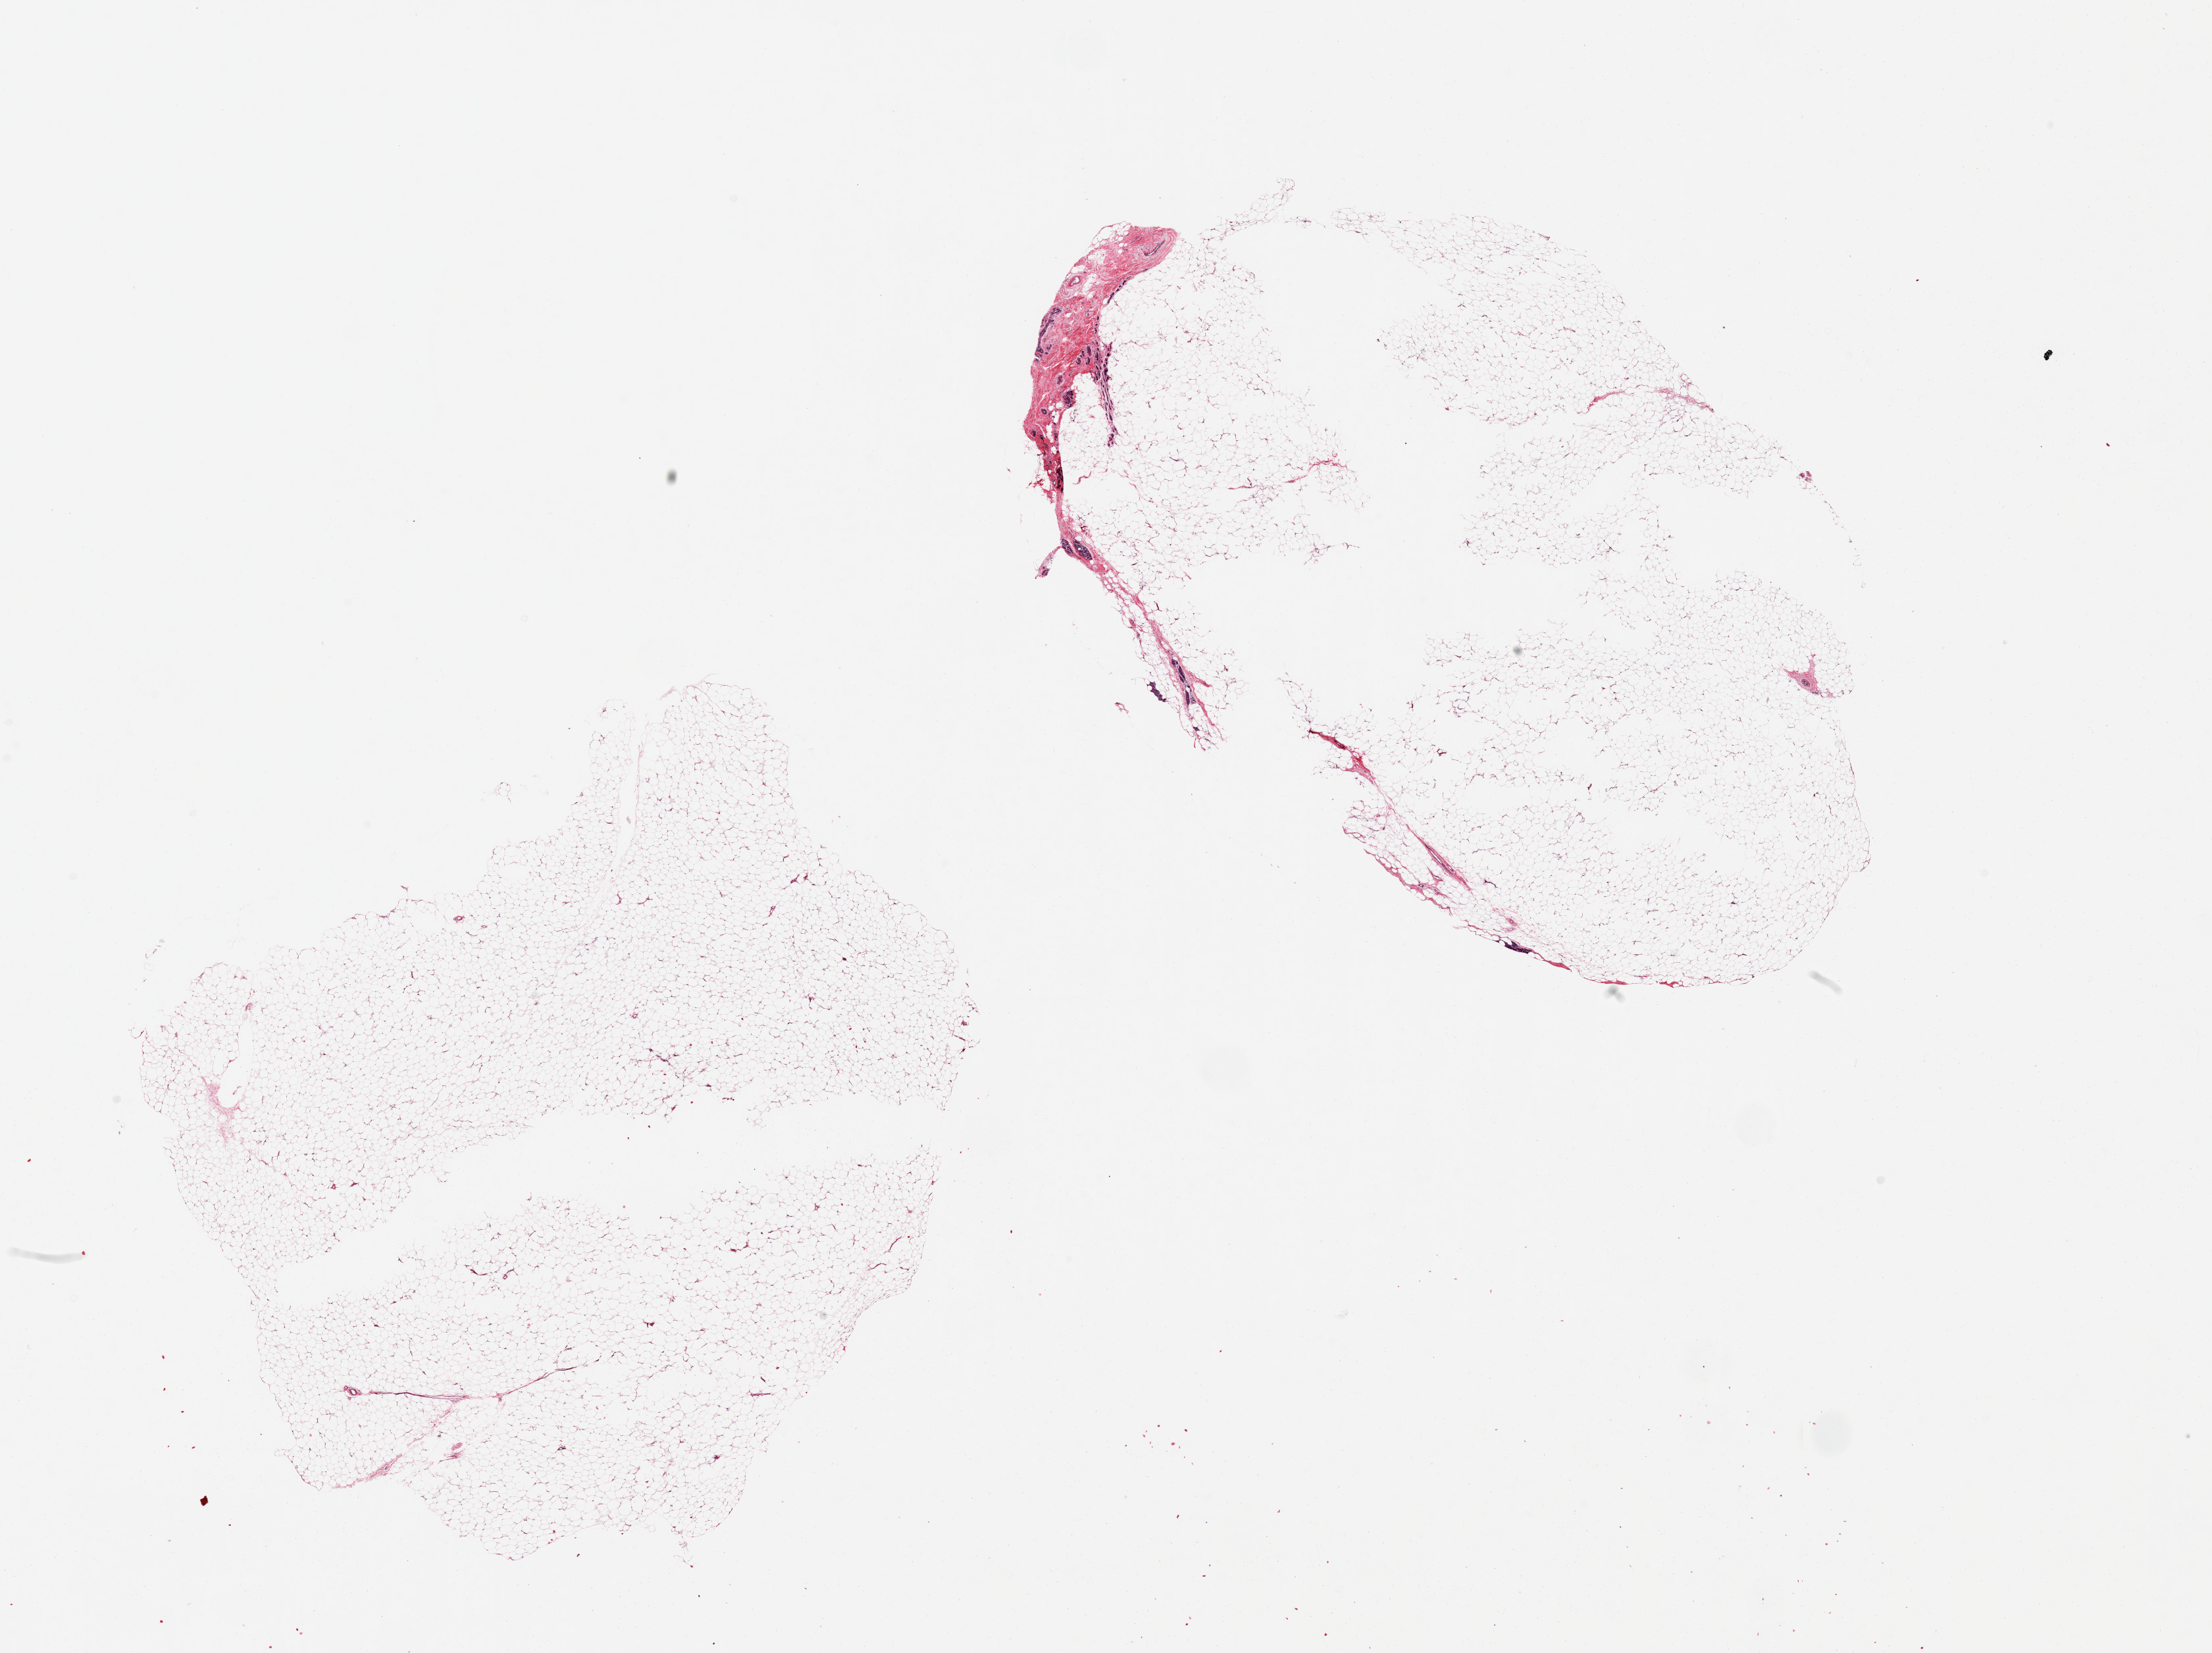
Digitized hematoxylin and eosin (H&E)-stained section, brightfield — a low-resolution overview of the entire scanned area, about 26.6 x 19.9 mm (slide scanned at 20x), PAXgene-fixed paraffin-embedded (PFPE) section, target tissue: breast, donor tissue sample.
Pathologist's review note for this sample: 2 pieces mainly adipose tissue; trace ductal elements in one section.